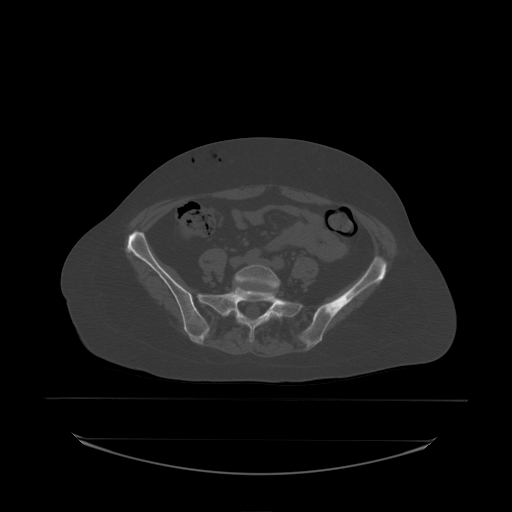
CT including the spine, one axial slice. Bone window (W 1800 / L 400 HU). 2.5 mm slice thickness. 512 × 512 image matrix. Patient: female, 53 years. From the clinical record (not read from this slice): primary cancer: lung.
Annotated regions visible in this slice (semi-automatically segmented with operator editing):
- L5 vertebra: bounding box [x1, y1, x2, y2] px = [235, 265, 281, 318]